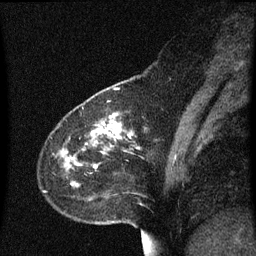
Breast MRI (dynamic contrast-enhanced), one sagittal slice. Position 19 of 60 along the scan axis. Dynamic contrast-enhanced series, image 2 of 3 at this slice position (ordered by acquisition). 1.5 T. TE 4.2 ms, TR 8.4 ms. 2 mm slice thickness. 256 × 256 image matrix. Patient: female, 49 years. From the clinical record (not read from this slice): setting: breast cancer imaged before/during neoadjuvant chemotherapy; receptor status: HR-positive, HER2-negative.
Outlined on this slice (semi-automatically segmented with operator editing):
- analysis volume of interest (the breast-tissue region the enhancement analysis was run in; not a lesion): bounding box [x1, y1, x2, y2] px = [44, 96, 147, 213]
- tumour enhancement mask (voxels above the 70 % enhancement threshold inside the analysis volume of interest): [93, 124, 120, 169]